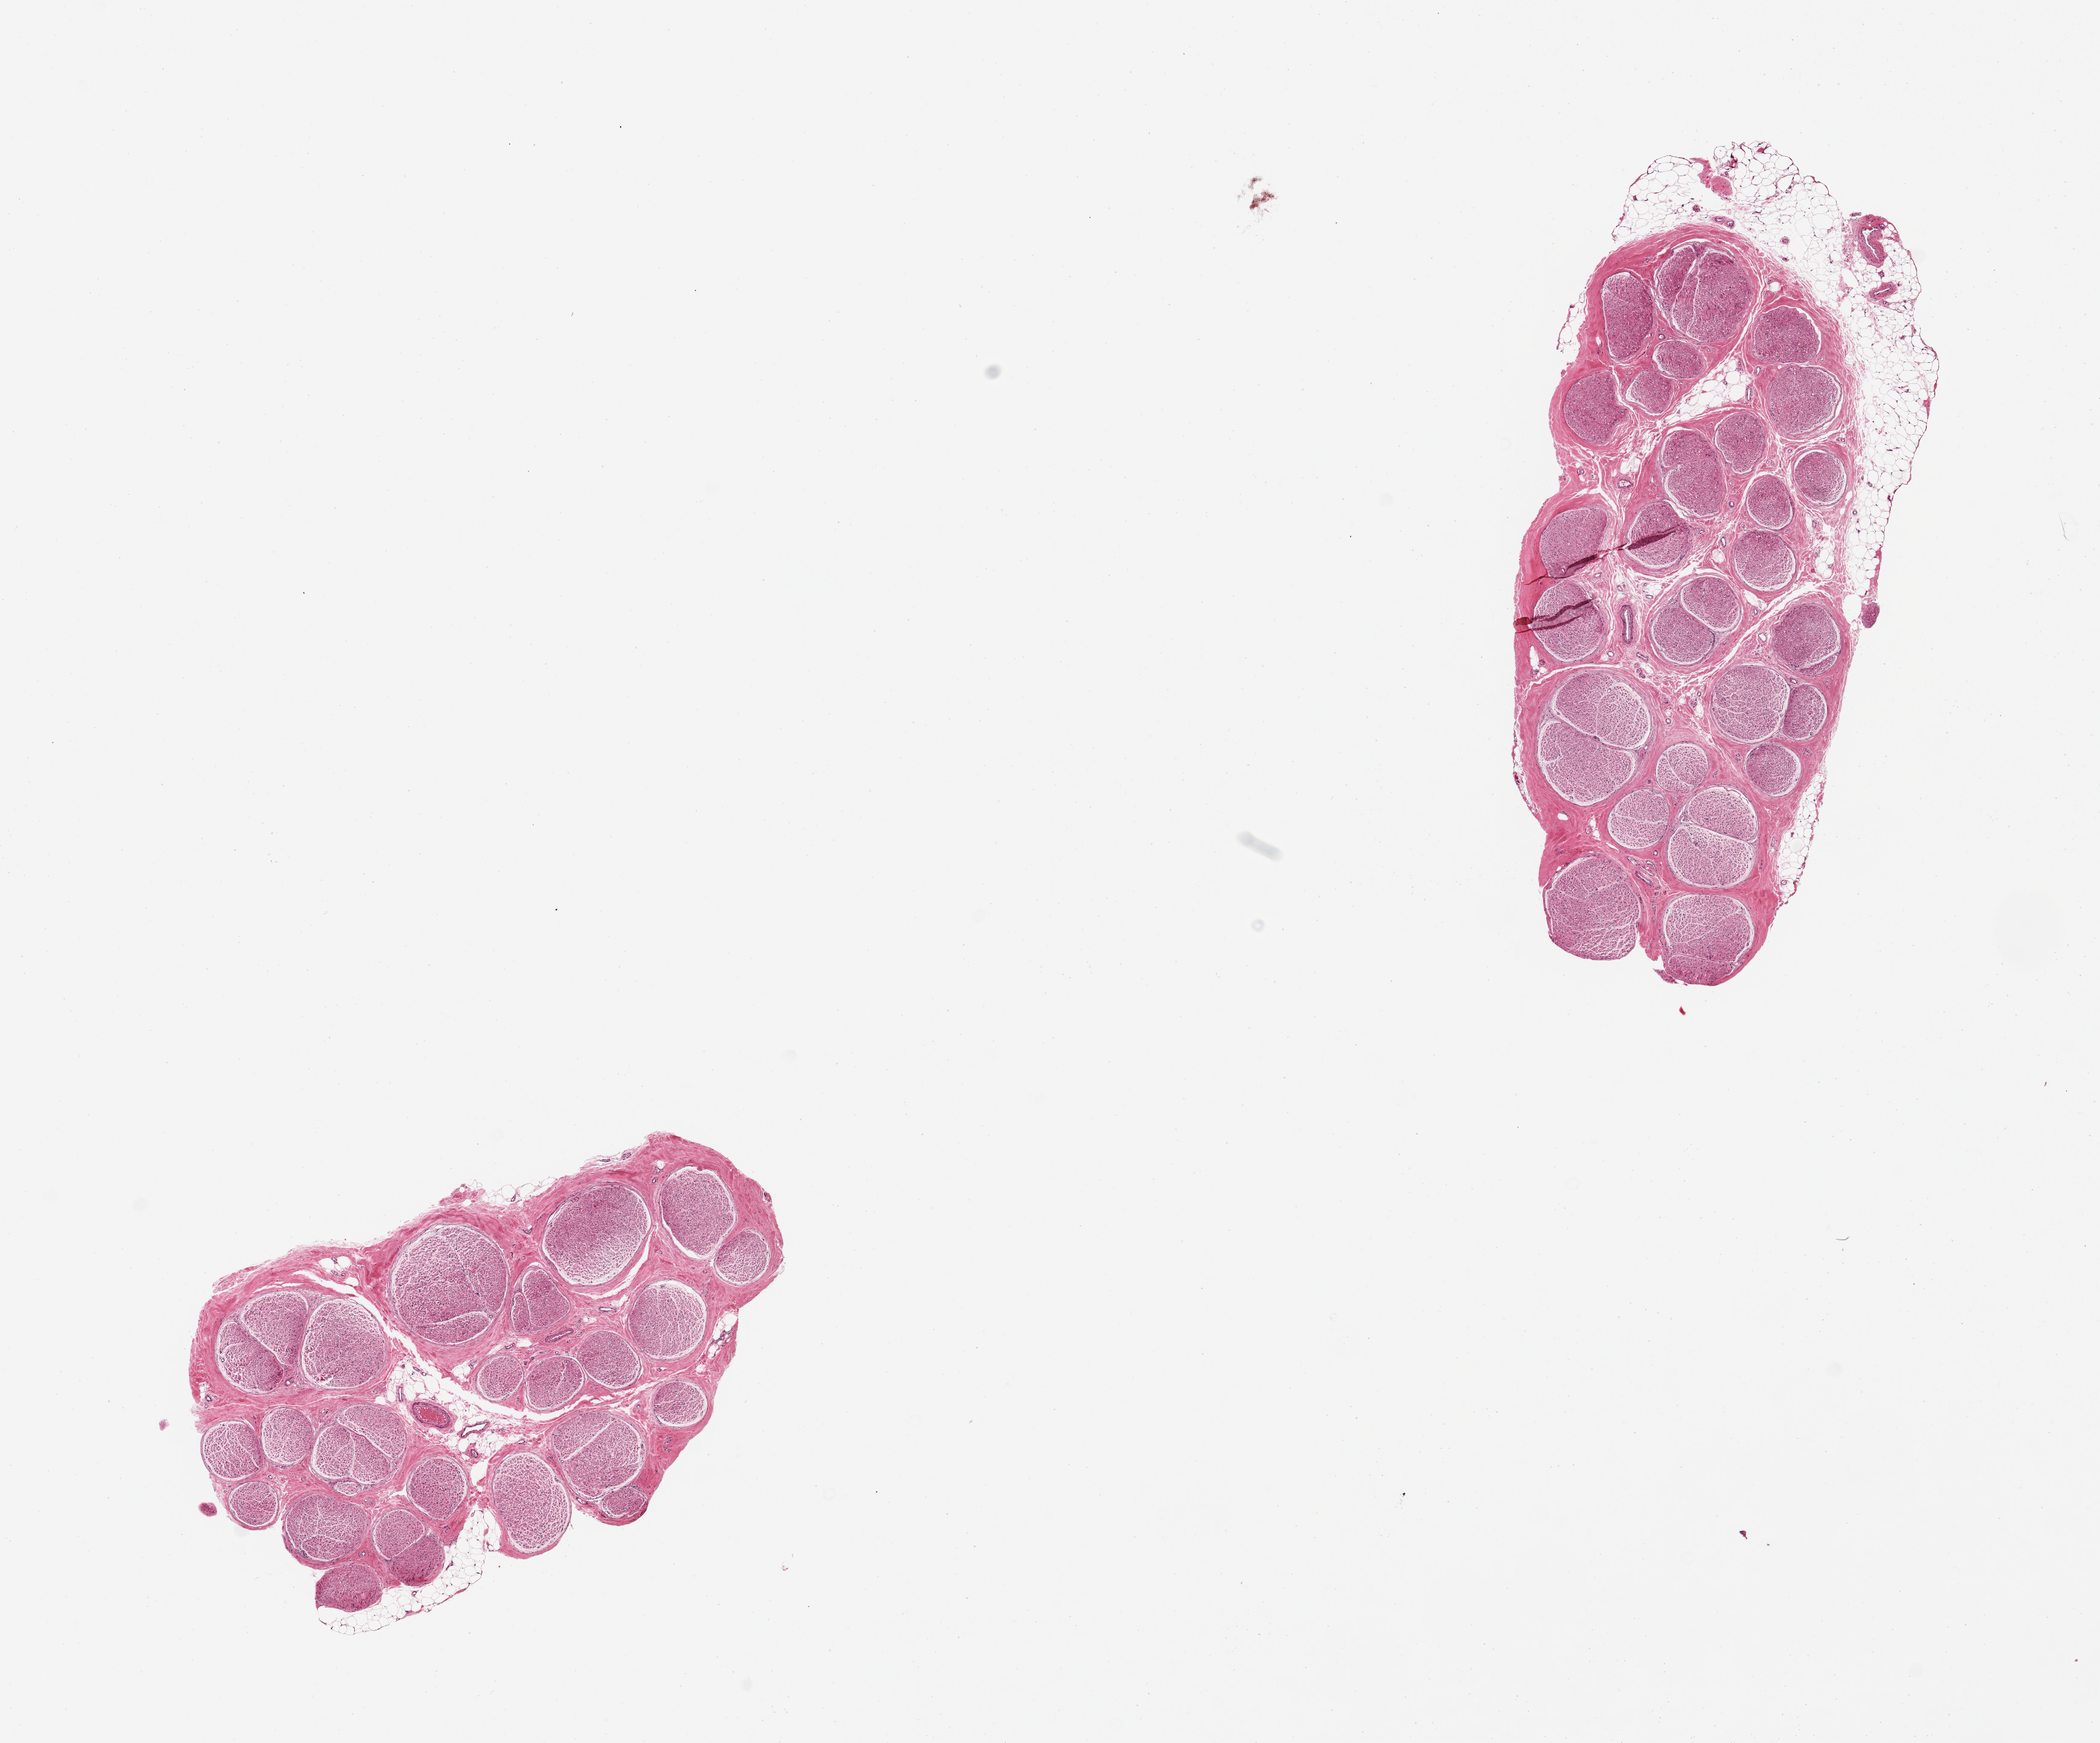
Haematoxylin and eosin whole-slide image, brightfield, low-resolution overview of the scanned area, about 13.8 x 11.4 mm (slide scanned at 20x). PAXgene-fixed, paraffin-embedded tissue. Sampled site (target tissue): tibial nerve. Donor tissue sample. Donor sex: female.
Review note (as recorded): 2 pieces, trace adherent fat up to ~0.5mm, good specimens.